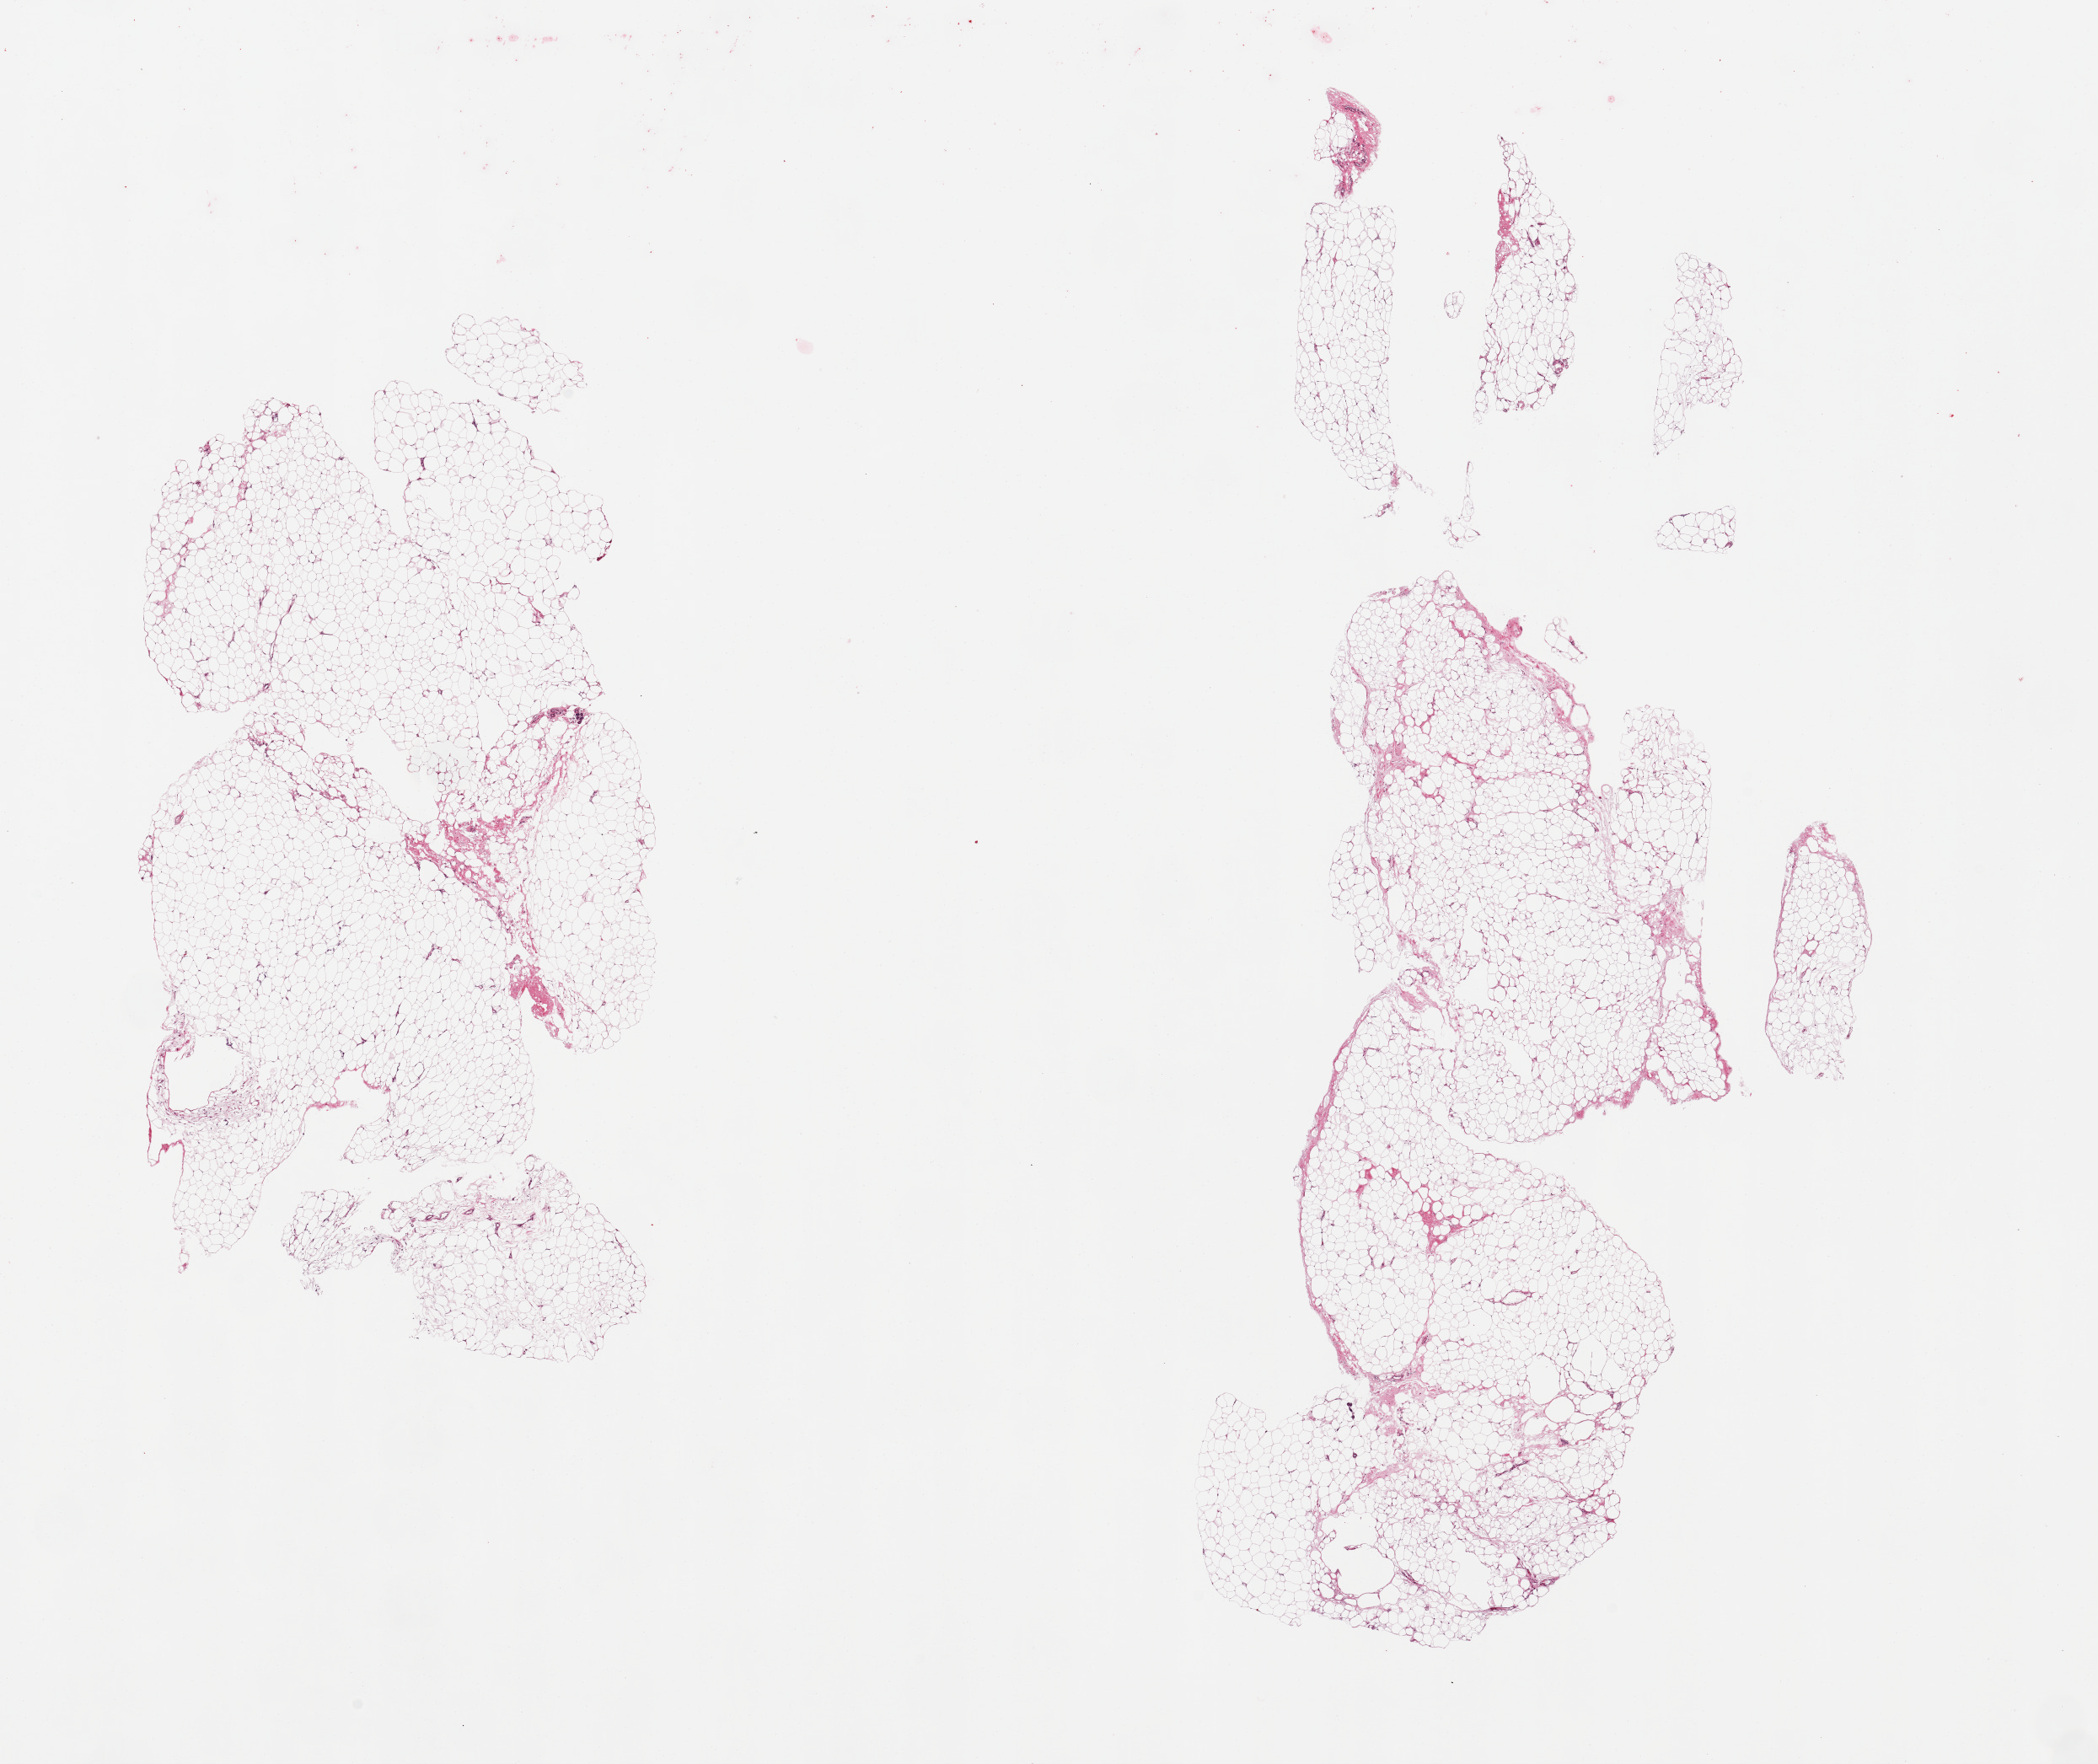
Whole-slide image, haematoxylin and eosin stain, low-resolution overview of the scanned area, about 19.7 x 16.6 mm. PAXgene-fixed, paraffin-embedded tissue. Target tissue: adipose tissue. Donor tissue sample.
Pathologist's review note for this sample: 2 pieces, minimal fascia/vascular elements.